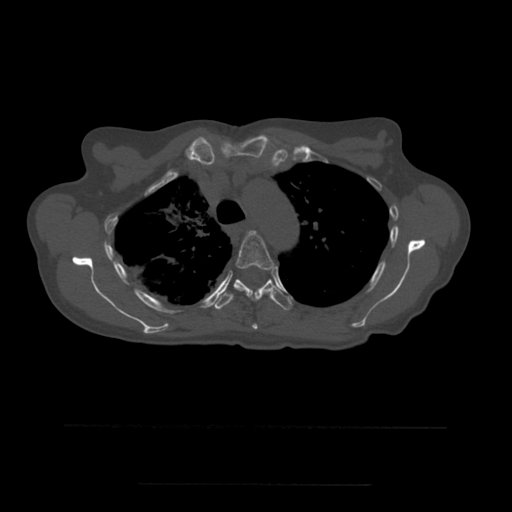
CT including the spine, one axial slice. Position 401 of 544 along the scan axis. Bone window (W 1800 / L 400 HU). 1.25 mm slice thickness. 512 × 512 image matrix, field of view 350 × 350 mm. Patient age 58 years. From the clinical record (not read from this slice): primary cancer: lung.
Annotated regions visible in this slice (semi-automatically segmented with operator editing):
- T4 vertebra: box from (x=236, y=231) to (x=274, y=330) px
- T5 vertebra: (x=215, y=279)–(x=292, y=311)